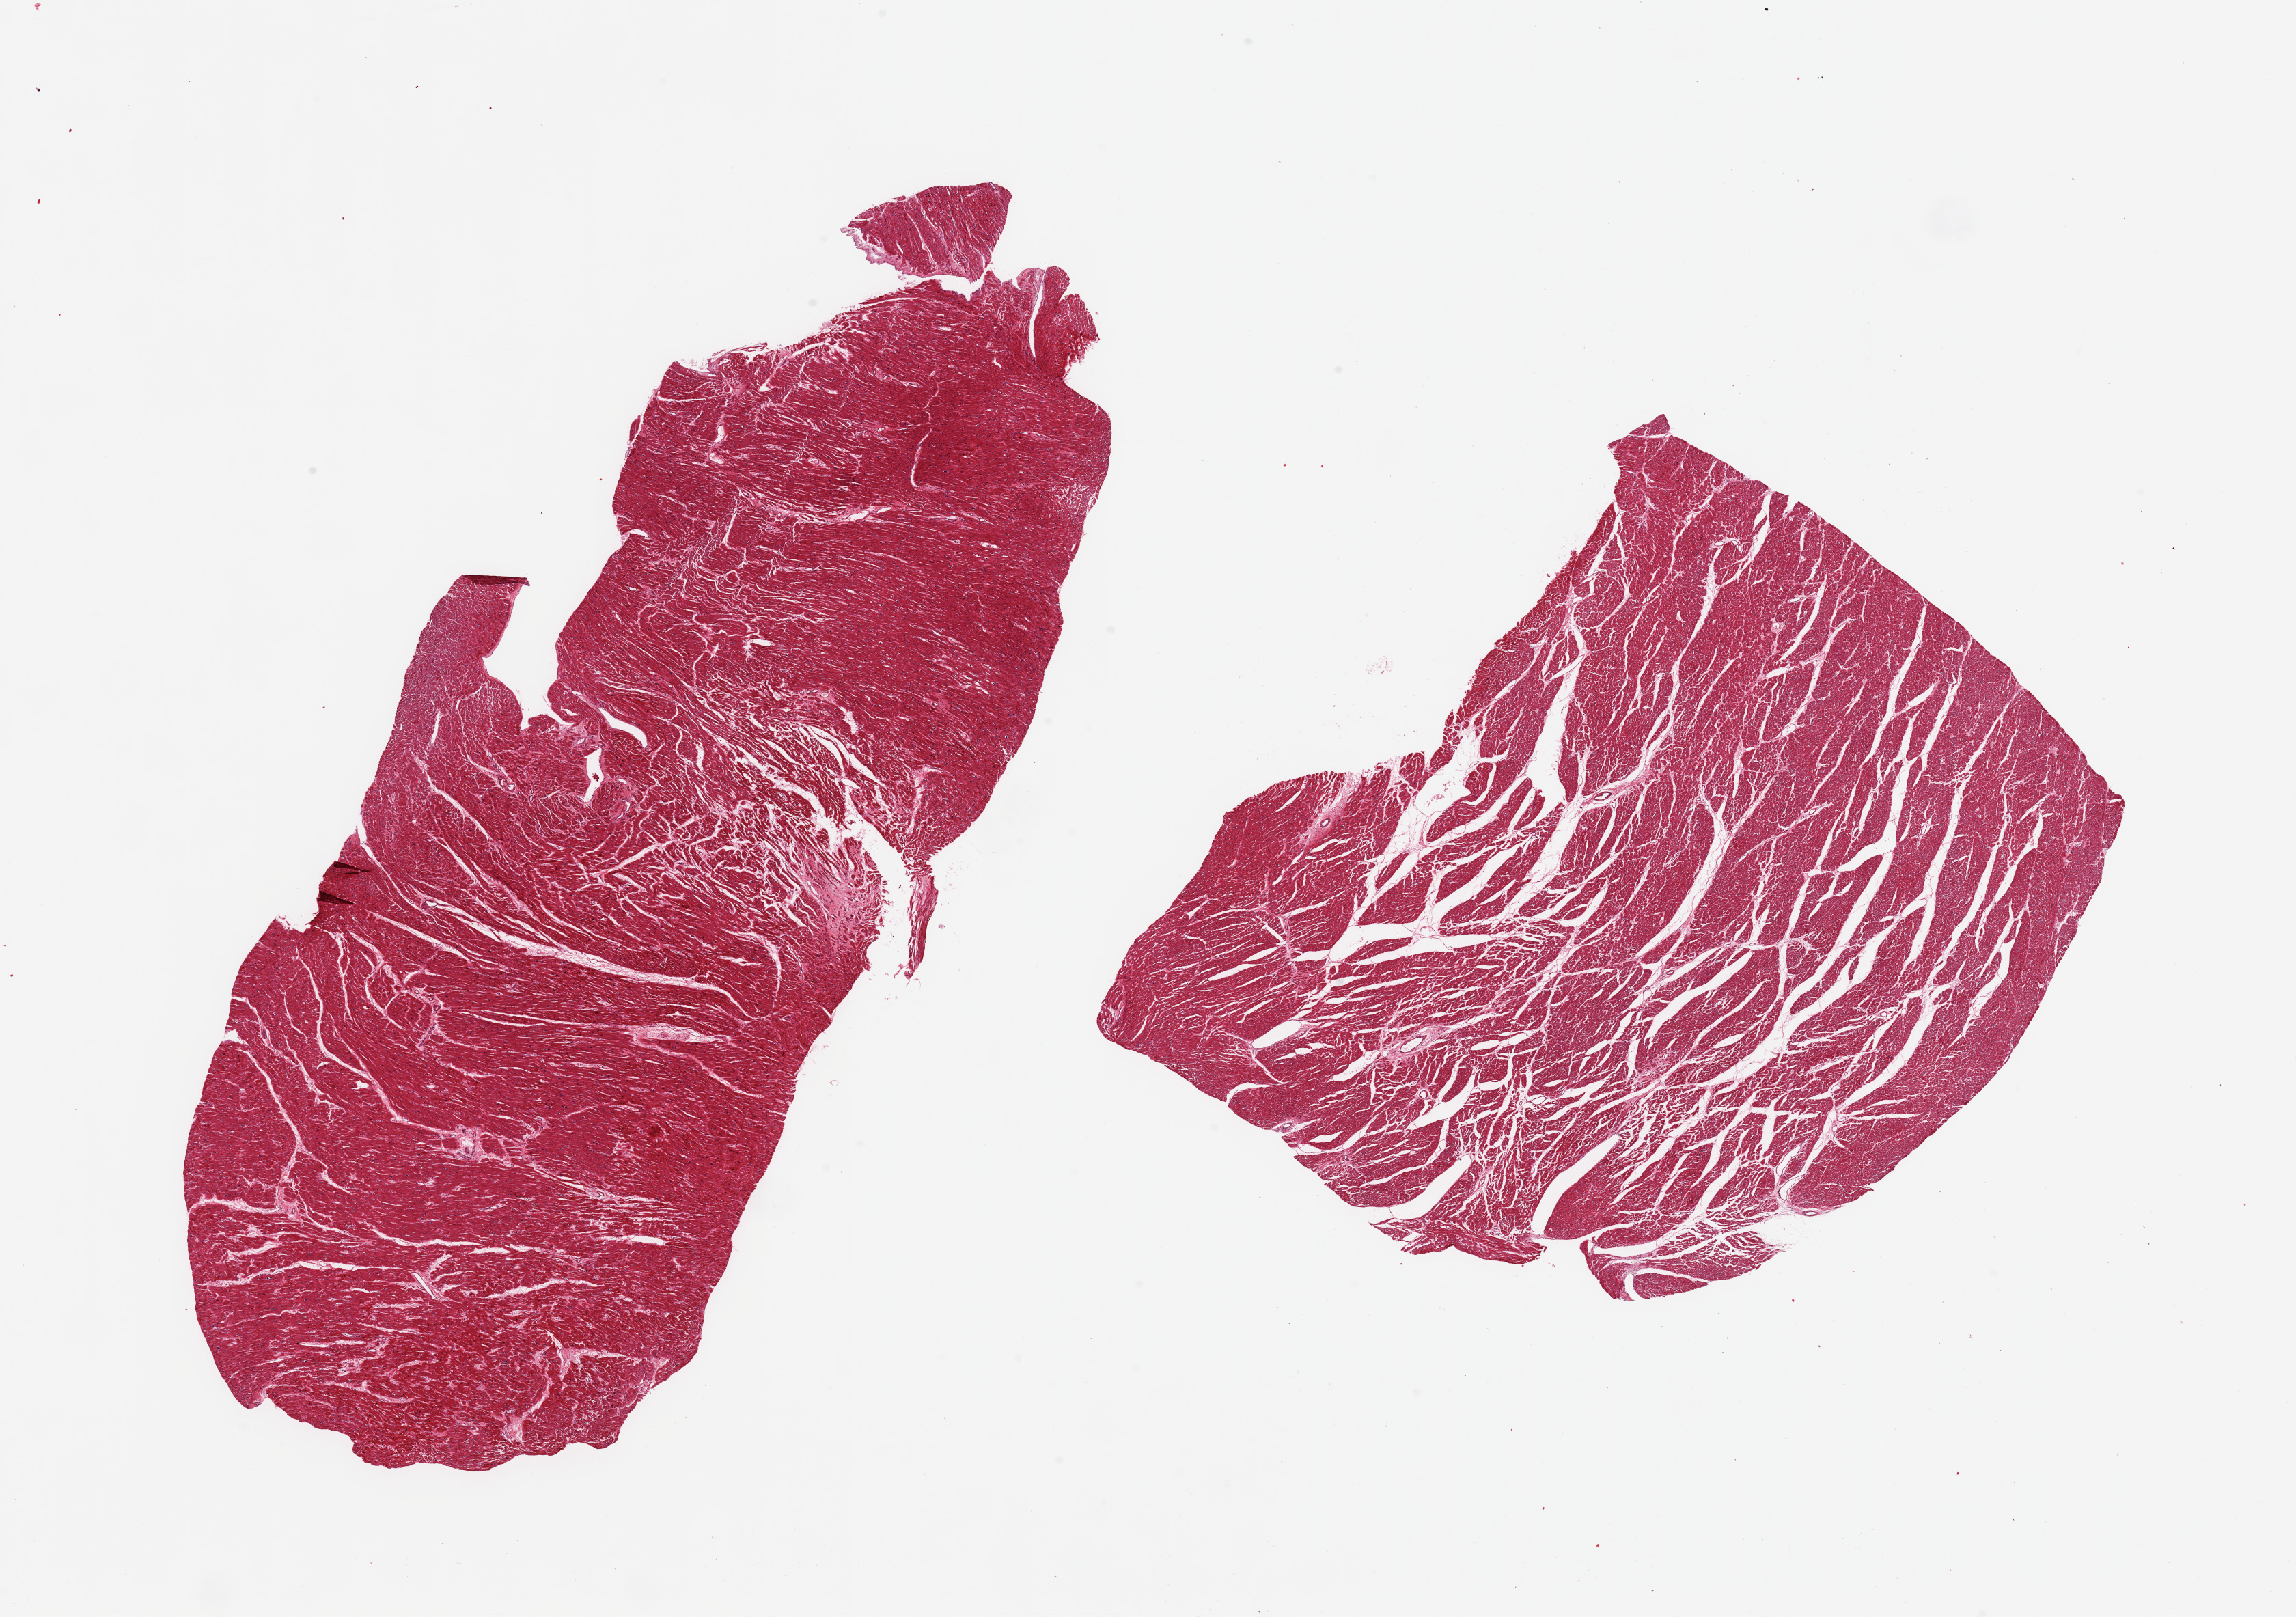
Hematoxylin and eosin (H&E) whole-slide image, brightfield — shown as a low-resolution overview of the whole scanned area (about 26.6 x 18.7 mm, from a 20x scan). PAXgene-fixed, paraffin-embedded tissue. Target tissue: heart. Donor tissue sample.
Review note (as recorded): 2 pieces, mild-moderate ischemic changes/fibrosis, microinfarct.